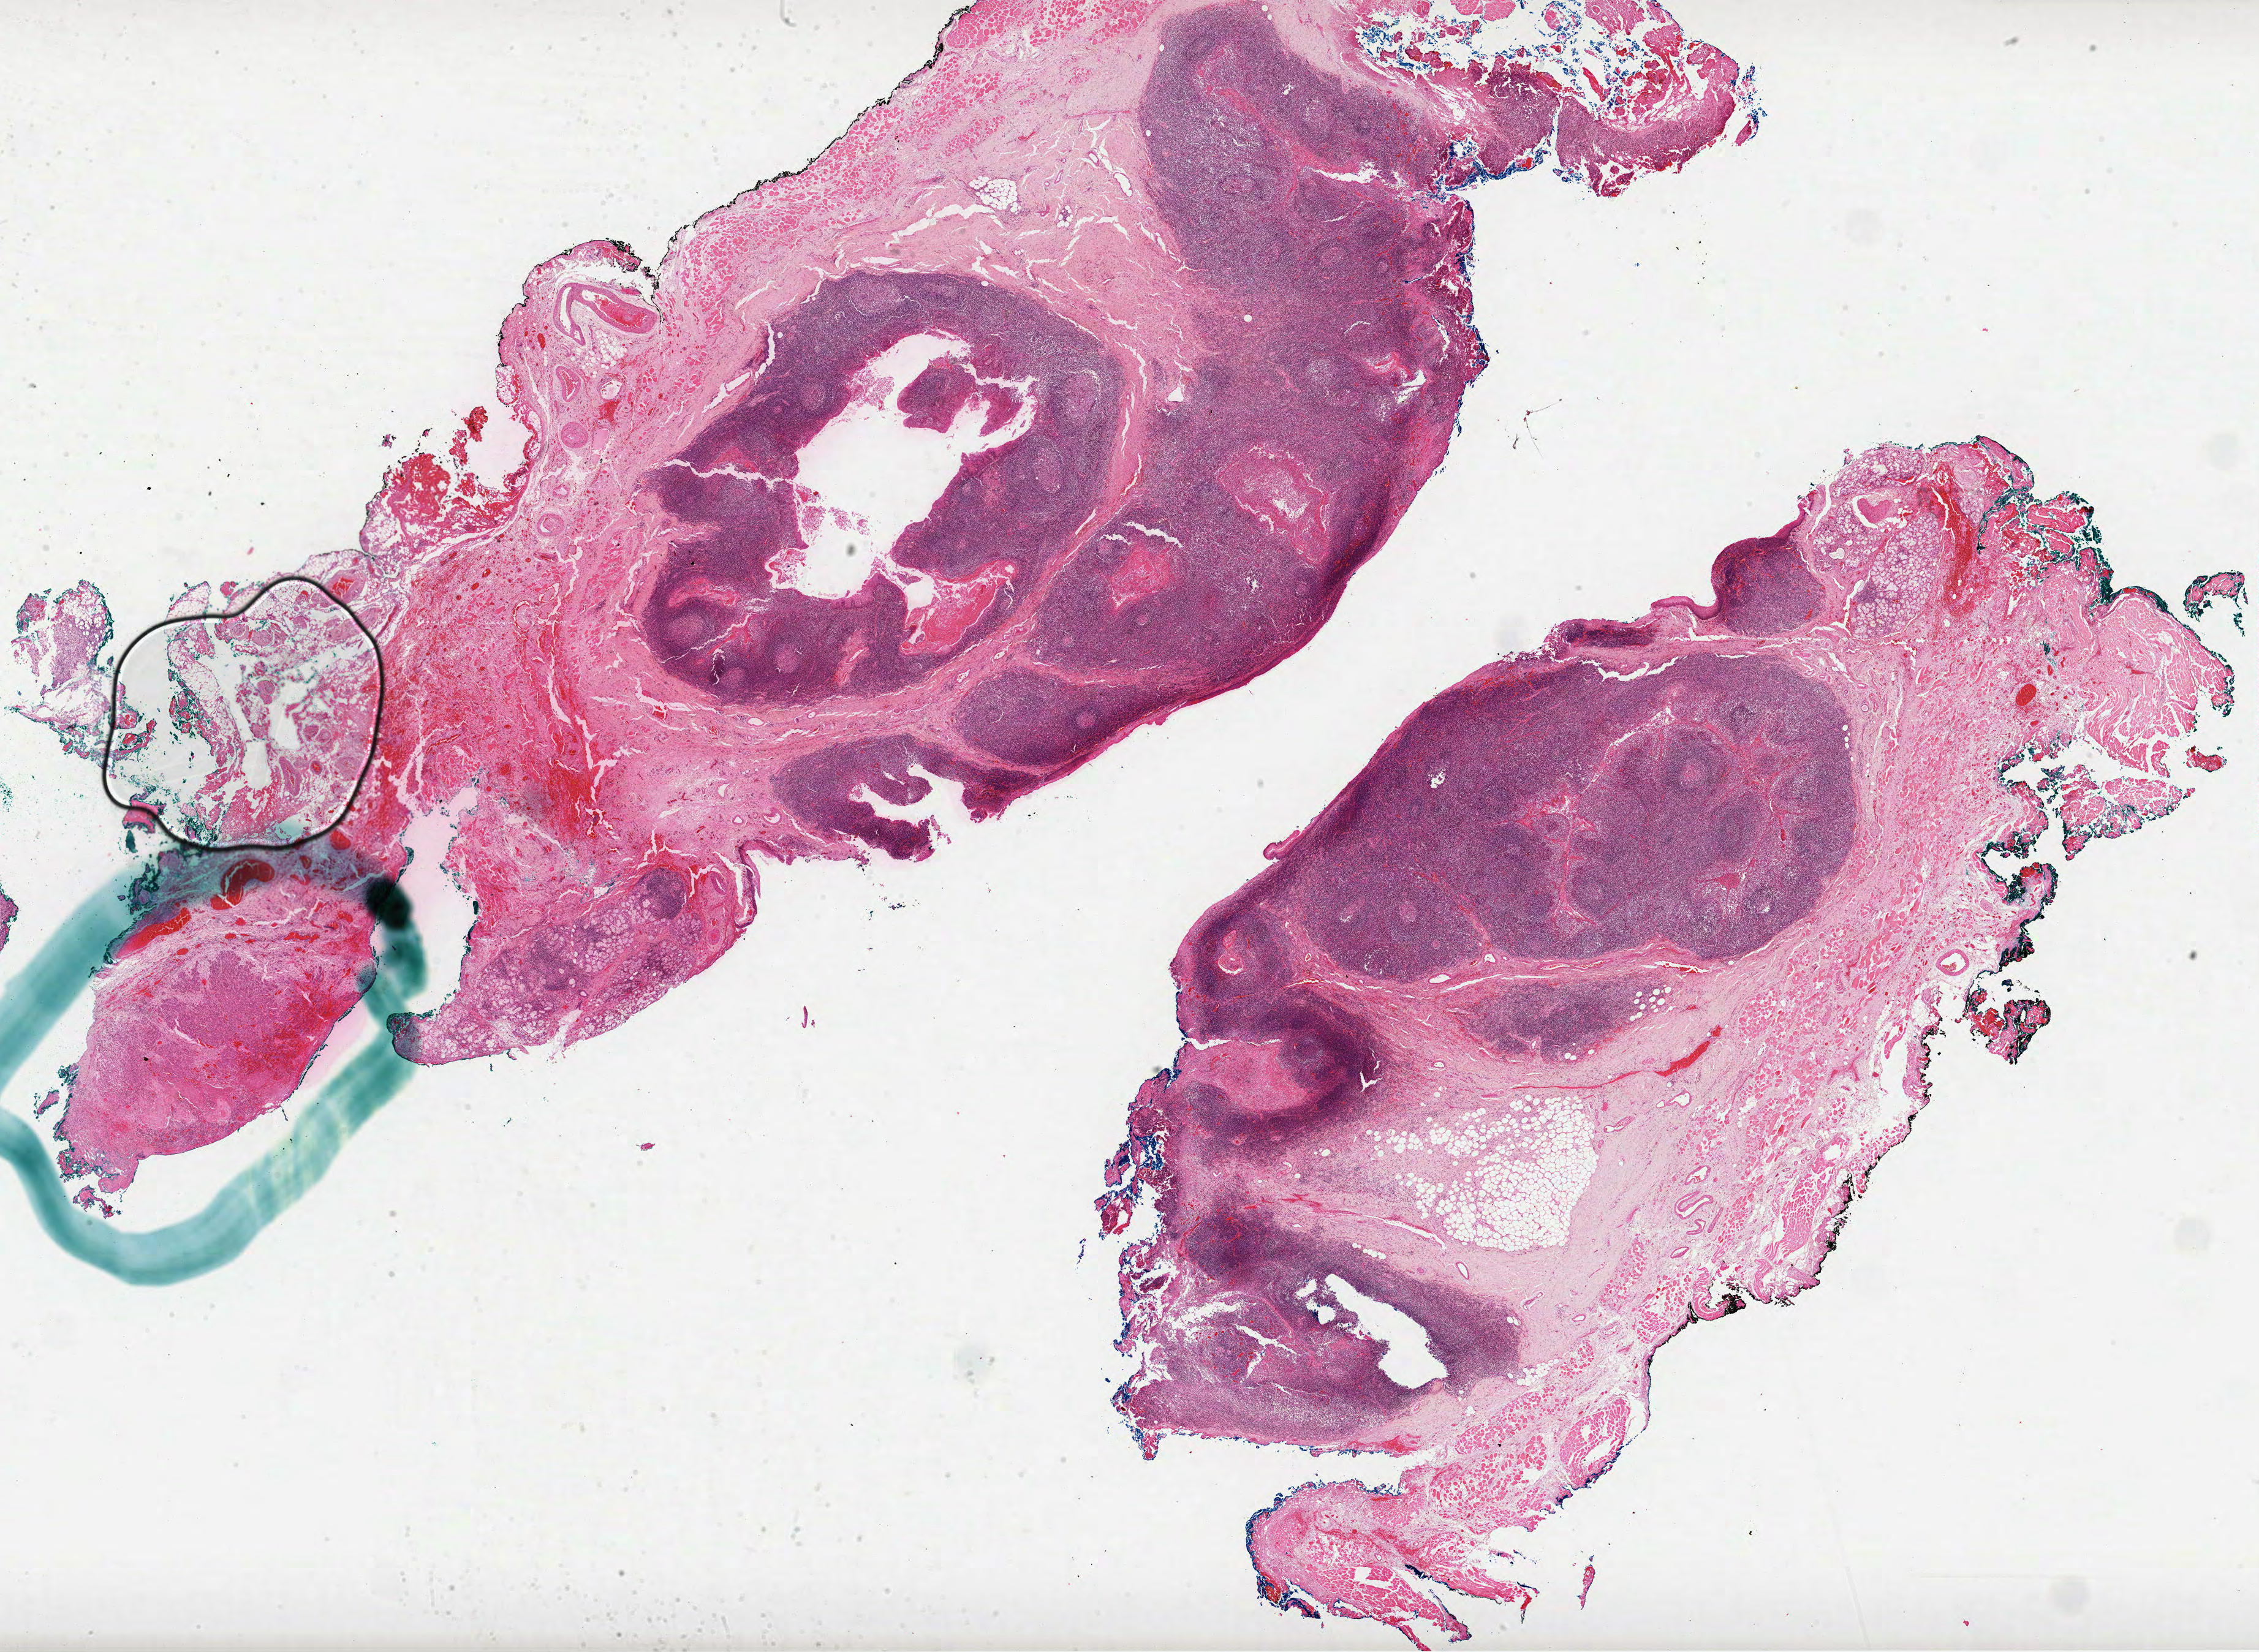
Whole-slide histology image, H&E — whole scanned area (about 29.7 x 21.7 mm, from a 40x scan) shown as a low-resolution overview. Formalin-fixed paraffin-embedded (FFPE) diagnostic section. Head and neck, primary tumour sample. Male patient; age at initial diagnosis 63 years. Histologic grade: G3 (poorly differentiated).
AJCC pathologic stage: I (7th edition). Histologic diagnosis: Squamous cell carcinoma, NOS.